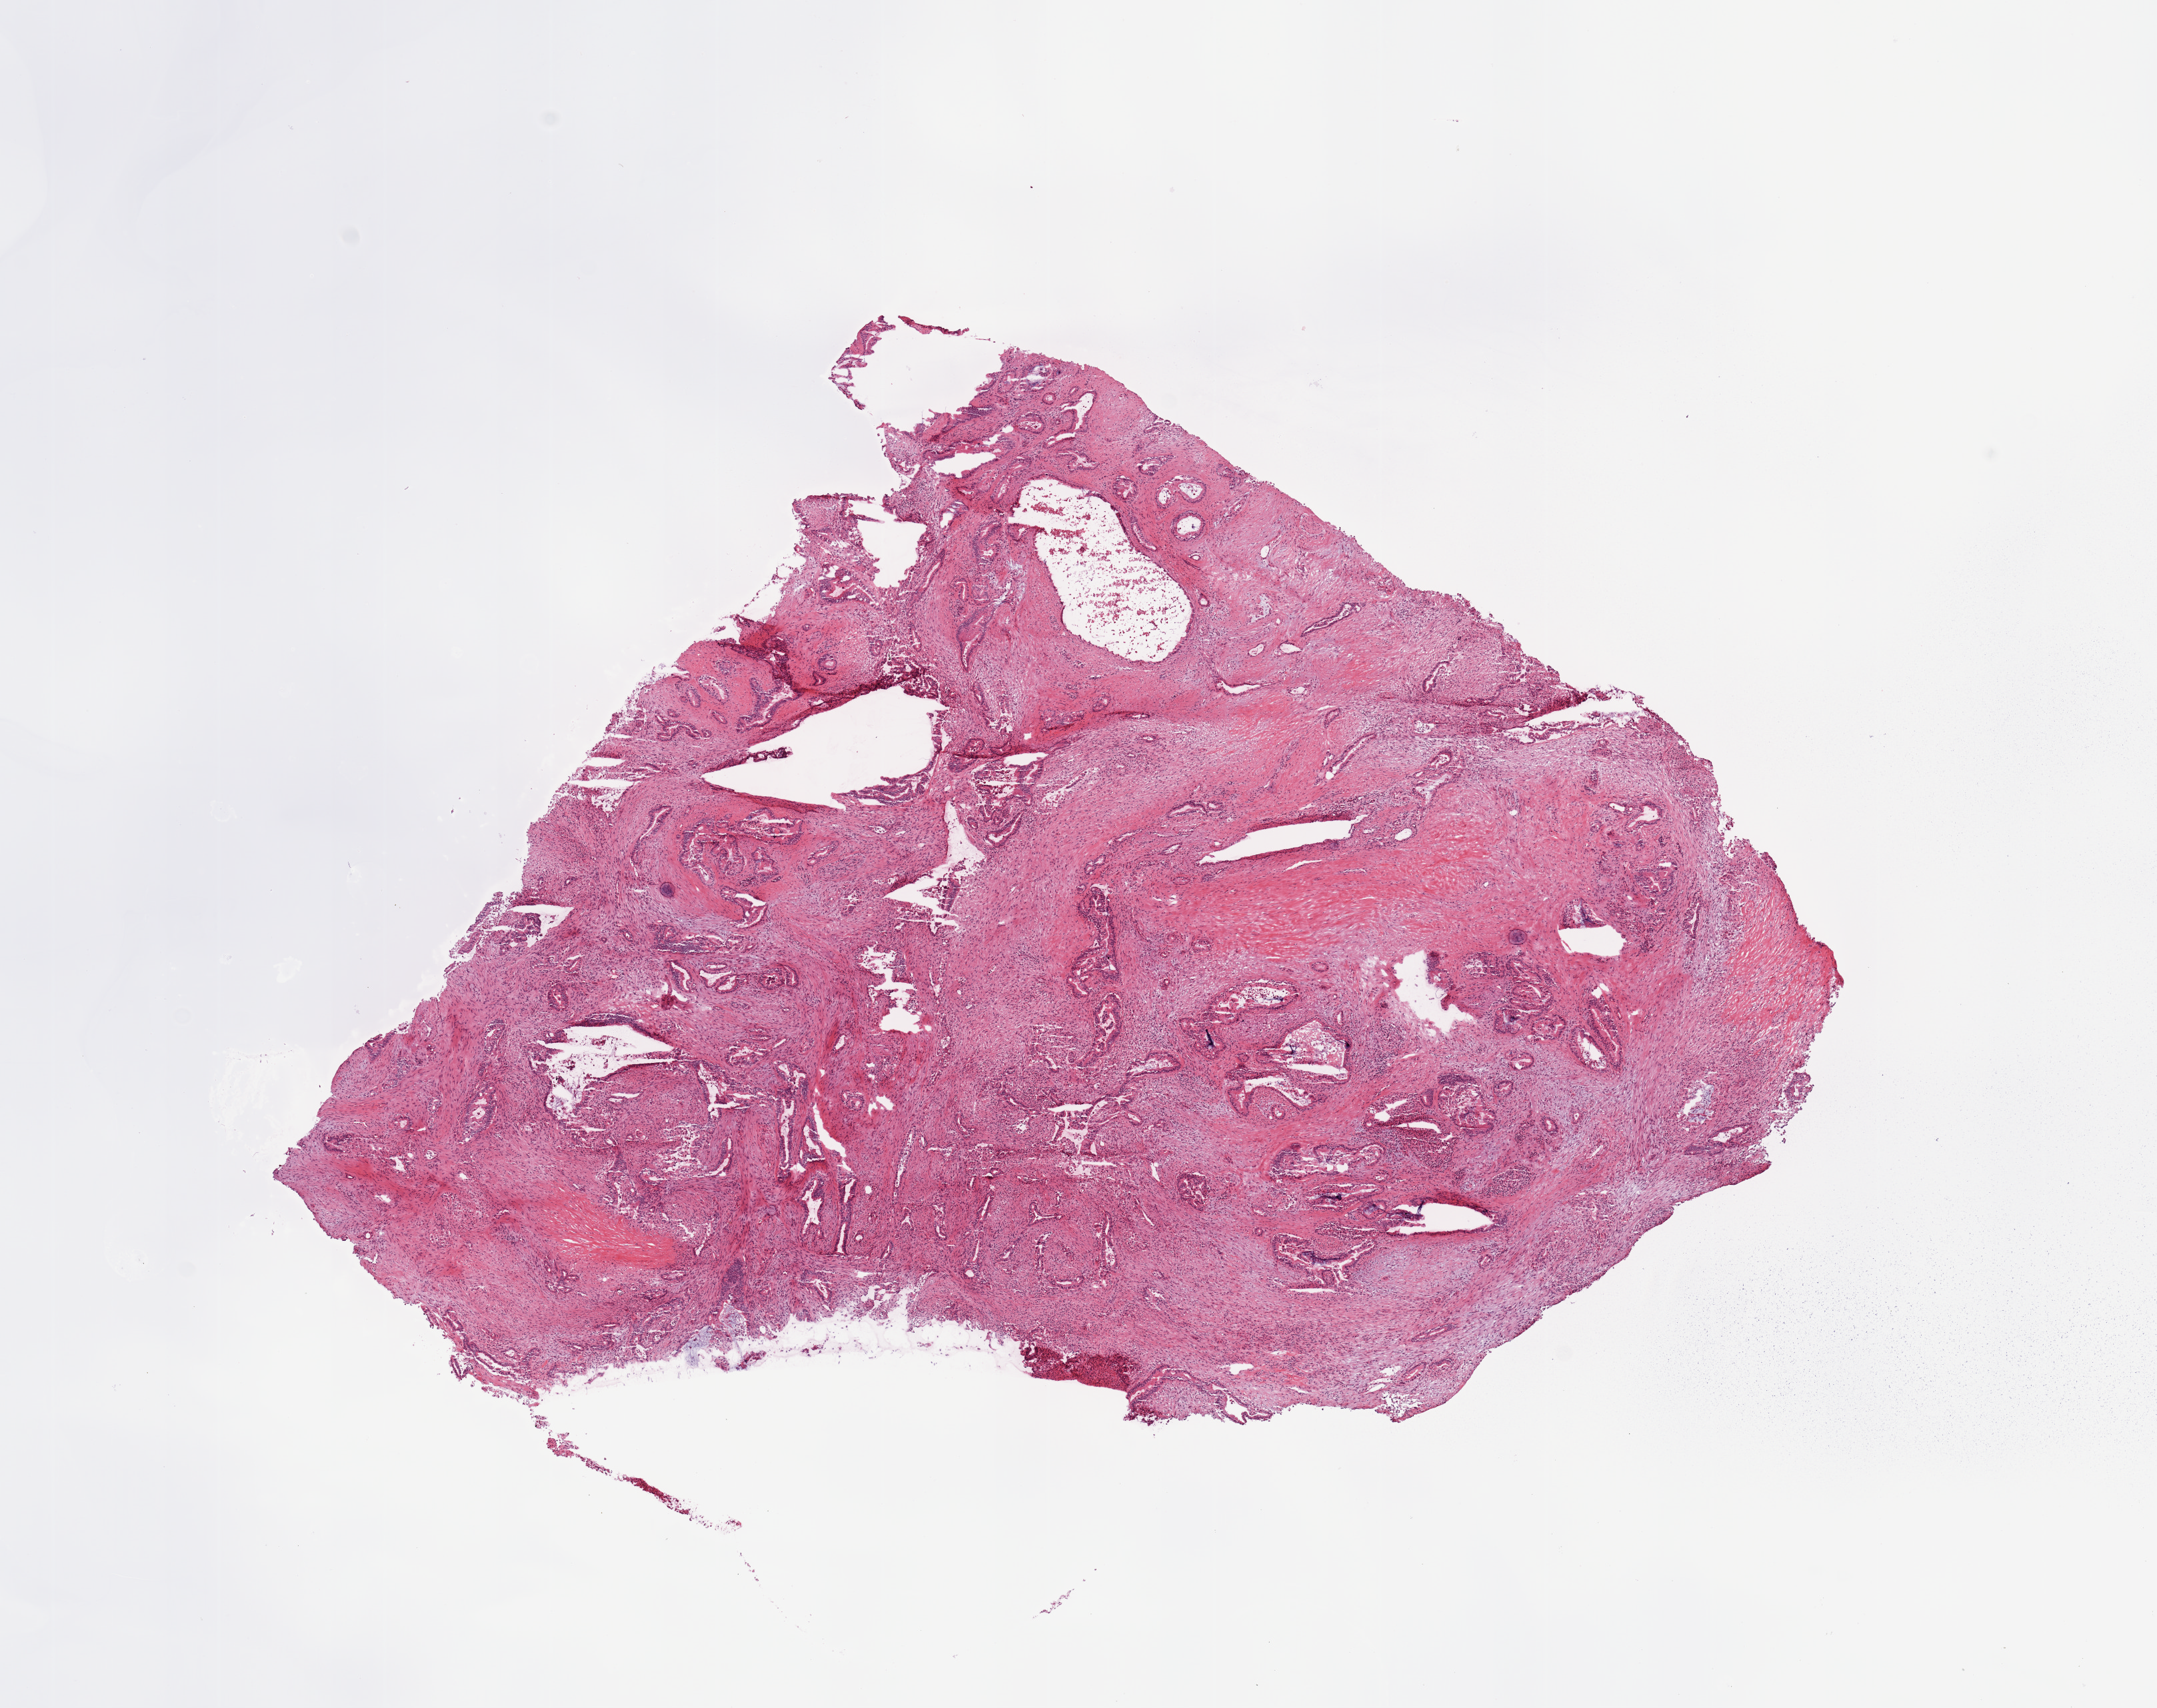
H&E-stained whole-slide image — a low-resolution overview of the entire scanned area, about 12.8 x 10.1 mm, pancreas, tumour tissue. Female, 59 y/o. Histologic grade: G2 (moderately differentiated).
• primary tumour site (as recorded): body
• AJCC pathologic stage: IIB
• histologic diagnosis: Infiltrating duct carcinoma, NOS